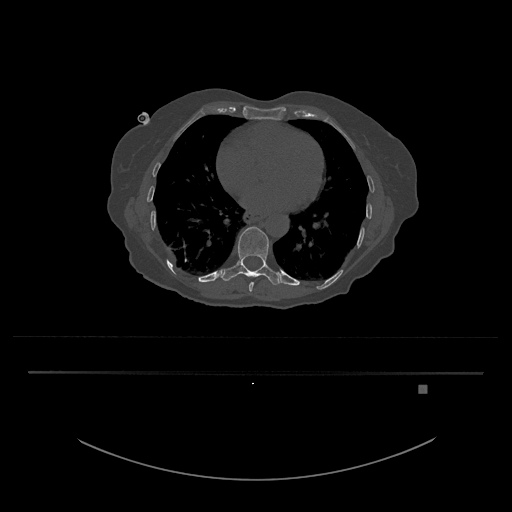
CT including the spine, one axial slice; slice 723 of 797 in the series (ordered by position); 120 kVp; bone window (W 1800 / L 400 HU); 512 × 512 image matrix, field of view 500 × 500 mm. Female patient, age 57 years. From the clinical record (not read from this slice): primary cancer: cervical.
Structures marked on this image (semi-automatic segmentation, software-assisted and operator-edited):
- T10 vertebra: bounding box [x1, y1, x2, y2] px = [221, 226, 284, 285]
- T9 vertebra: [249, 282, 254, 292]